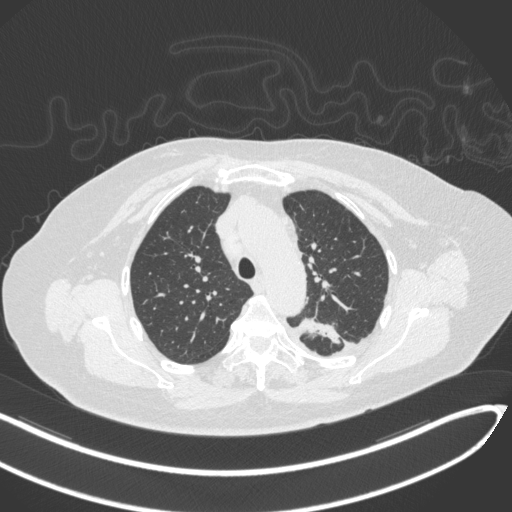
Chest CT, one axial slice; position 234 of 270 along the scan axis; reconstruction kernel B31f; 120 kVp; lung window (W 1500 / L -600 HU); 1 mm slice thickness; 512 × 512 image matrix, field of view 400 × 400 mm. Patient: female, 76 years. Case-level facts recorded for this patient, not image findings: clinical TNM (as recorded): T1c N0 M0.
Annotated regions visible in this slice (bounding box drawn by a radiologist):
- lung tumour (recorded histology: adenocarcinoma): box from (x=296, y=312) to (x=342, y=346) px